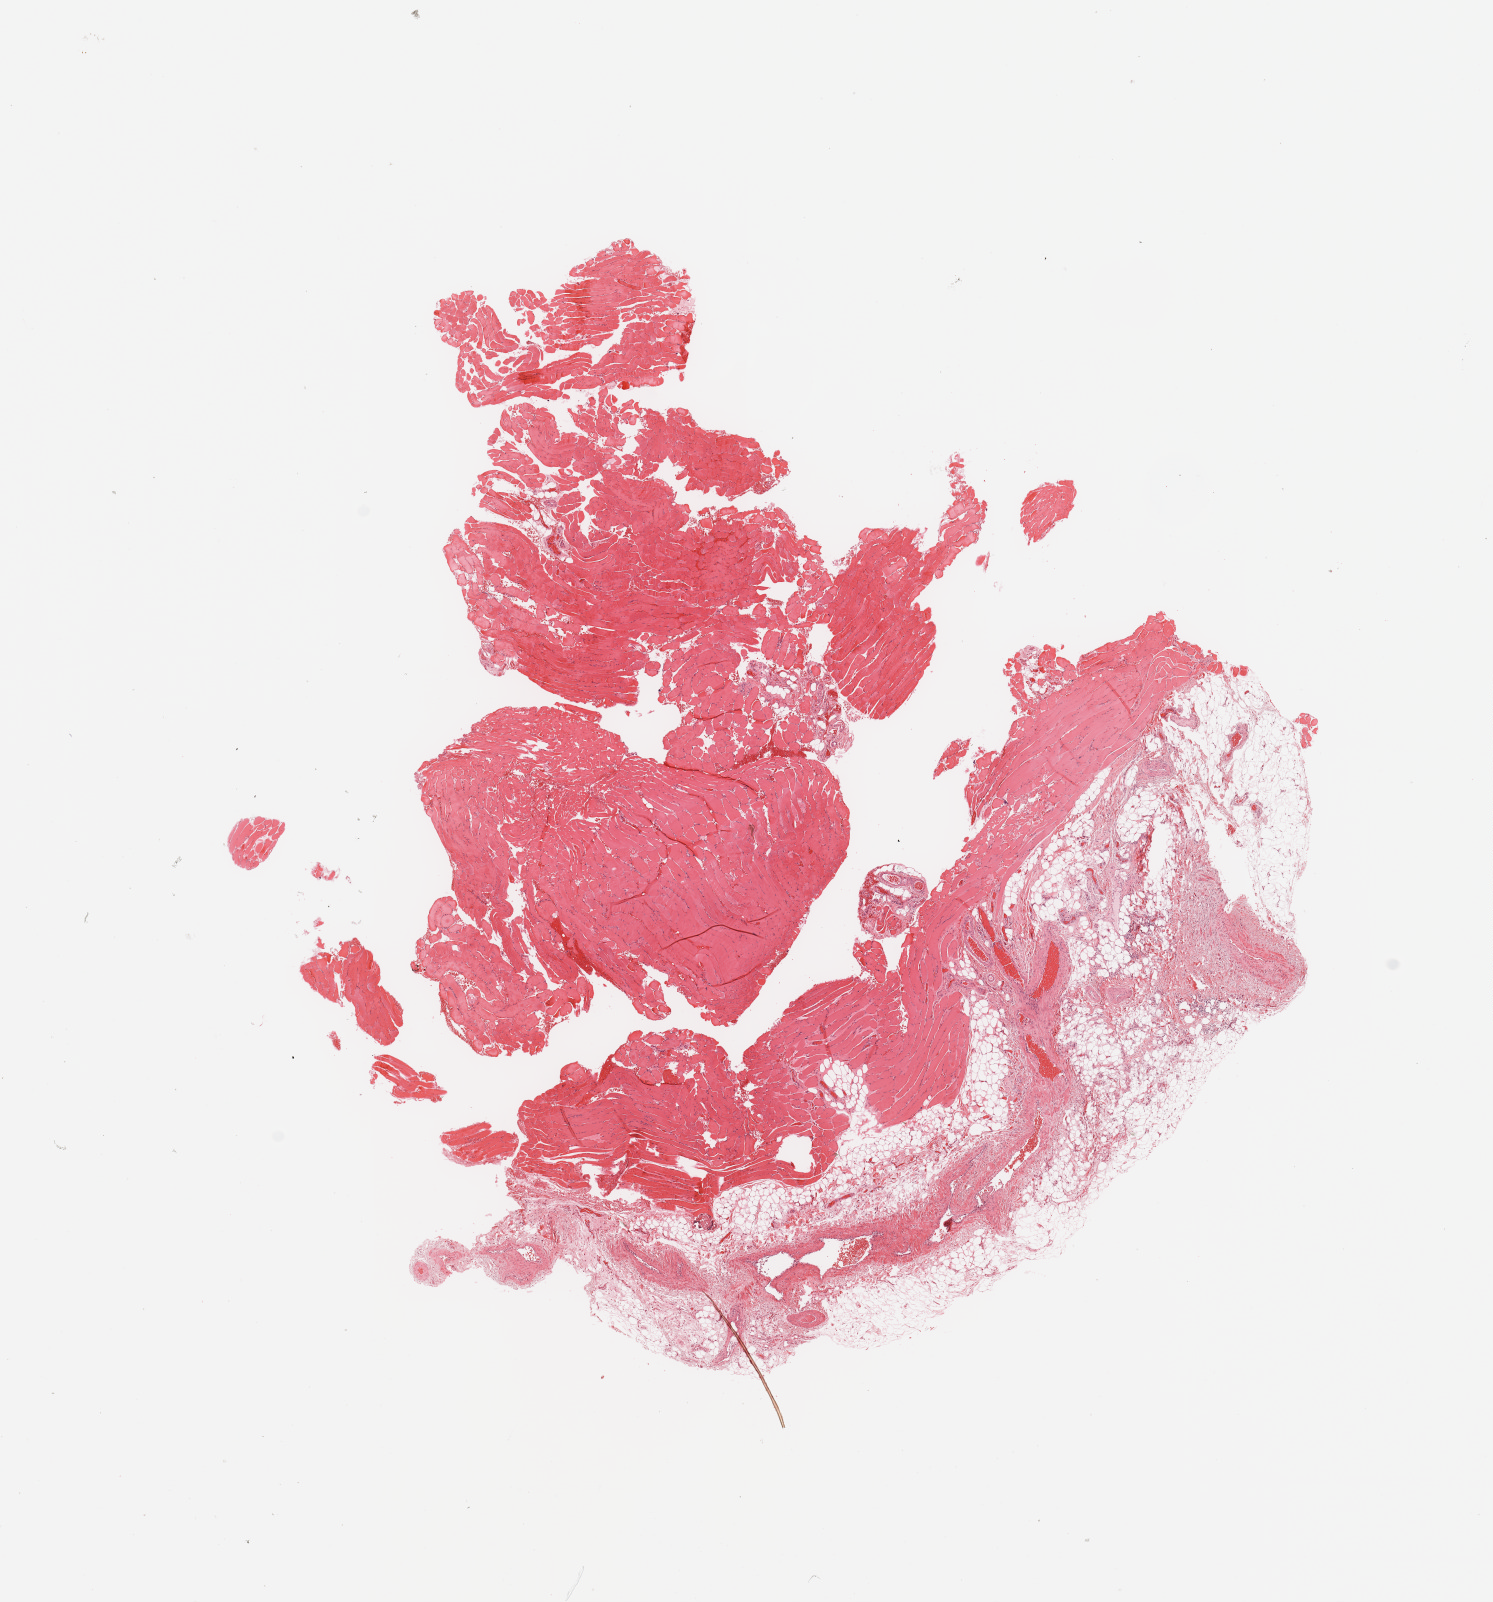
H&E whole-slide image, a low-resolution overview of the entire scanned area, about 11.8 x 12.7 mm (from a 20x scan). Normal (non-tumour) tissue sample. Patient: female, age 51 years.
This section: normal (non-tumour) tissue from the same patient. Patient diagnosis (cohort enrolment): sarcoma (site not recorded at cohort level).